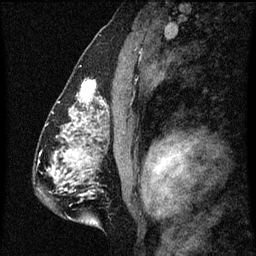
Breast MRI (dynamic contrast-enhanced), one sagittal slice; slice 37 of 60 in the series (ordered by position); dynamic contrast-enhanced series, image 2 of 3 at this slice position (ordered by acquisition); 1.5 T; TE 4.2 ms, TR 8 ms; 2 mm slice thickness; 256 × 256 image matrix, field of view 180 × 180 mm. Female patient, age 51 years.
Outlined on this slice (semi-automatically segmented with operator editing):
- analysis volume of interest (the breast-tissue region the enhancement analysis was run in; not a lesion): bounding box (x1, y1, x2, y2) in pixels: (61, 80, 102, 129)
- tumour enhancement mask (voxels above the 70 % enhancement threshold inside the analysis volume of interest): (71, 80, 102, 127)